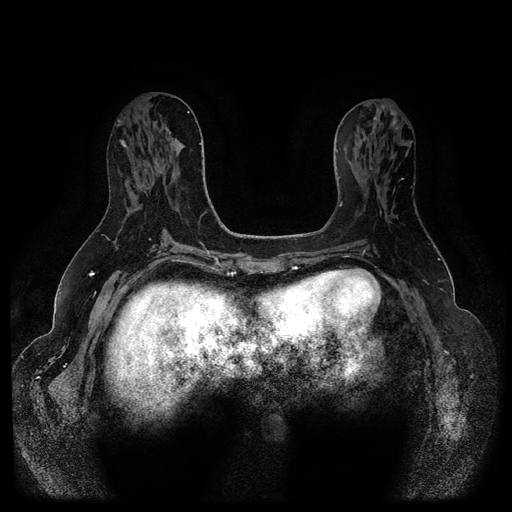
Breast MRI (dynamic contrast-enhanced, multi-phase), one axial slice. Position 45 of 116 along the scan axis. Dynamic contrast-enhanced series, time point 2 of 5 at this slice position (early post-contrast). 1.5 T. TE 2.6 ms, TR 5.3 ms. 512 × 512 image matrix. Female patient, age 54 years.
Outlined on this slice (semi-automatically segmented with operator editing):
- breast lesion (labelled benign in the annotation): box from (x=119, y=139) to (x=128, y=149) px